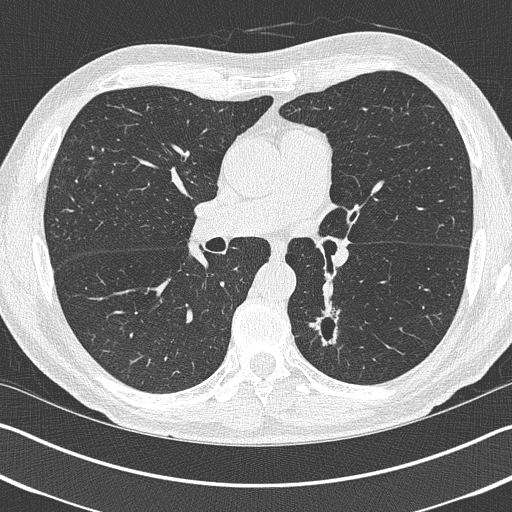
Low-dose screening chest CT, one axial slice. Slice 231 of 402 in the series (ordered by position). Reconstruction kernel B50f. 120 kVp. Lung window (W 1500 / L -600 HU). 1 mm slice thickness. 512 × 512 image matrix, field of view 340 × 340 mm.
Annotated regions visible in this slice (manually delineated by an expert):
- lesion 1 (tumor, lower lobe of left lung): bounding box [x1, y1, x2, y2] px = [310, 302, 340, 346]